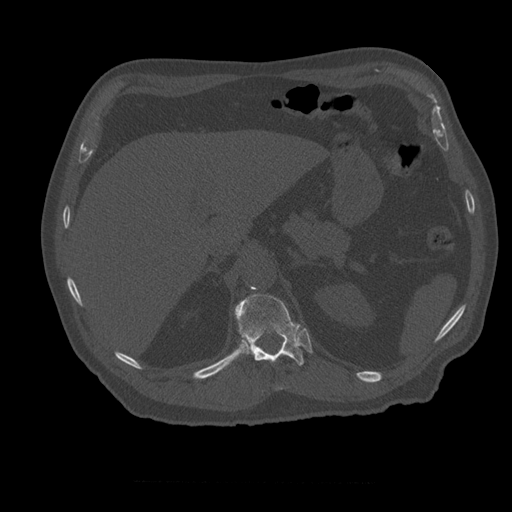
CT including the spine, one axial slice; slice 262 of 399 in the series (ordered by position); reconstruction kernel STANDARD; 120 kVp; bone window (W 1800 / L 400 HU); 1.25 mm slice thickness; 512 × 512 image matrix, field of view 407 × 407 mm. Patient age 73 years. Case-level facts recorded for this patient, not image findings: primary cancer: prostate; vertebrae with lytic lesions (as recorded): L2.
Annotated regions visible in this slice (semi-automatic segmentation, software-assisted and operator-edited):
- T12 vertebra: bounding box <235,294,305,366> (left, top, right, bottom; pixels)